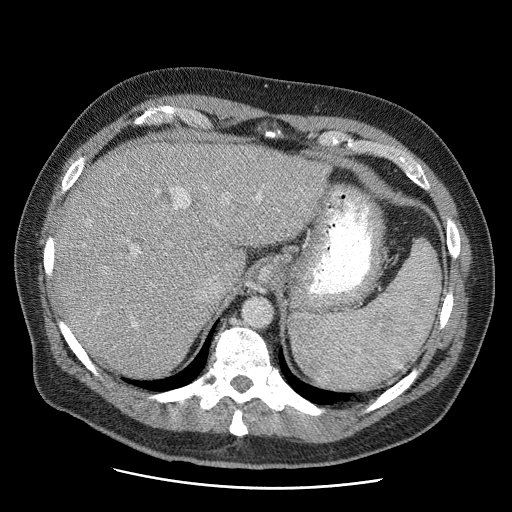
Contrast-enhanced abdominal CT (liver protocol), one axial slice; slice 42 of 81 in the series (ordered by position); 120 kVp; soft-tissue window (W 400 / L 40 HU); 2.5 mm slice thickness; 512 × 512 image matrix. From the clinical record (not read from this slice): diagnosis: hepatocellular carcinoma (patient treated with transarterial chemoembolisation; whether this scan precedes or follows treatment is not stated here); TNM stage (as recorded): Stage-IIIA; Child-Pugh class: A; tumour differentiation: moderately differentiated; tumour nodularity: multinodular.
Annotated regions visible in this slice (semi-automatically segmented with operator editing):
- liver parenchyma outside the tumour (the mass and vessels are separate outlines, so this box may not span the whole liver): bounding box <54,140,328,376> (left, top, right, bottom; pixels)
- liver vessels: <98,188,261,327>